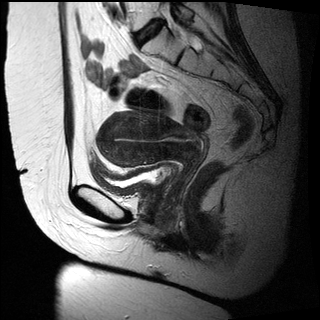
Pelvic MRI for cervical cancer, one sagittal slice. Slice 16 of 27 in the series (ordered by position). T2-weighted. 1.5 T. TE 89 ms, TR 2740 ms. 320 × 320 image matrix. Female patient, age 47 years.
Structures marked on this image (manually delineated by an expert):
- uterus and cervix: bounding box (x1, y1, x2, y2) in pixels: (98, 112, 203, 168)